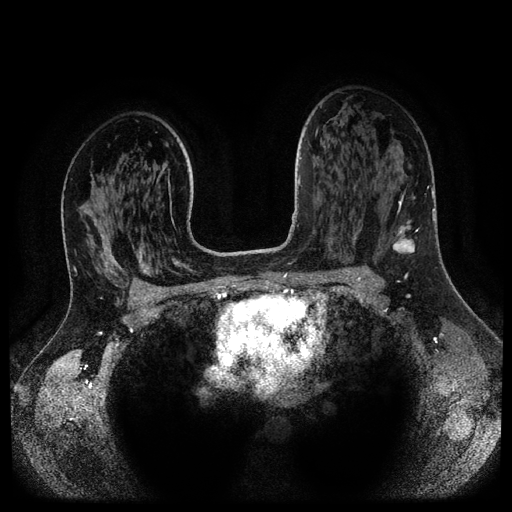
Breast MRI (dynamic contrast-enhanced, multi-phase), one axial slice; position 68 of 116 along the scan axis; dynamic contrast-enhanced series, time point 2 of 5 at this slice position (early post-contrast); 1.5 T; TE 2.6 ms, TR 5.3 ms; 2.1 mm slice thickness; 512 × 512 image matrix, field of view 360 × 360 mm. Patient: female, 37 years.
Outlined on this slice (semi-automatic segmentation, software-assisted and operator-edited):
- breast lesion (labelled 'tumour' in the annotation; benign lesions carry a separate 'benign' label): bounding box <392,220,415,254> (left, top, right, bottom; pixels)